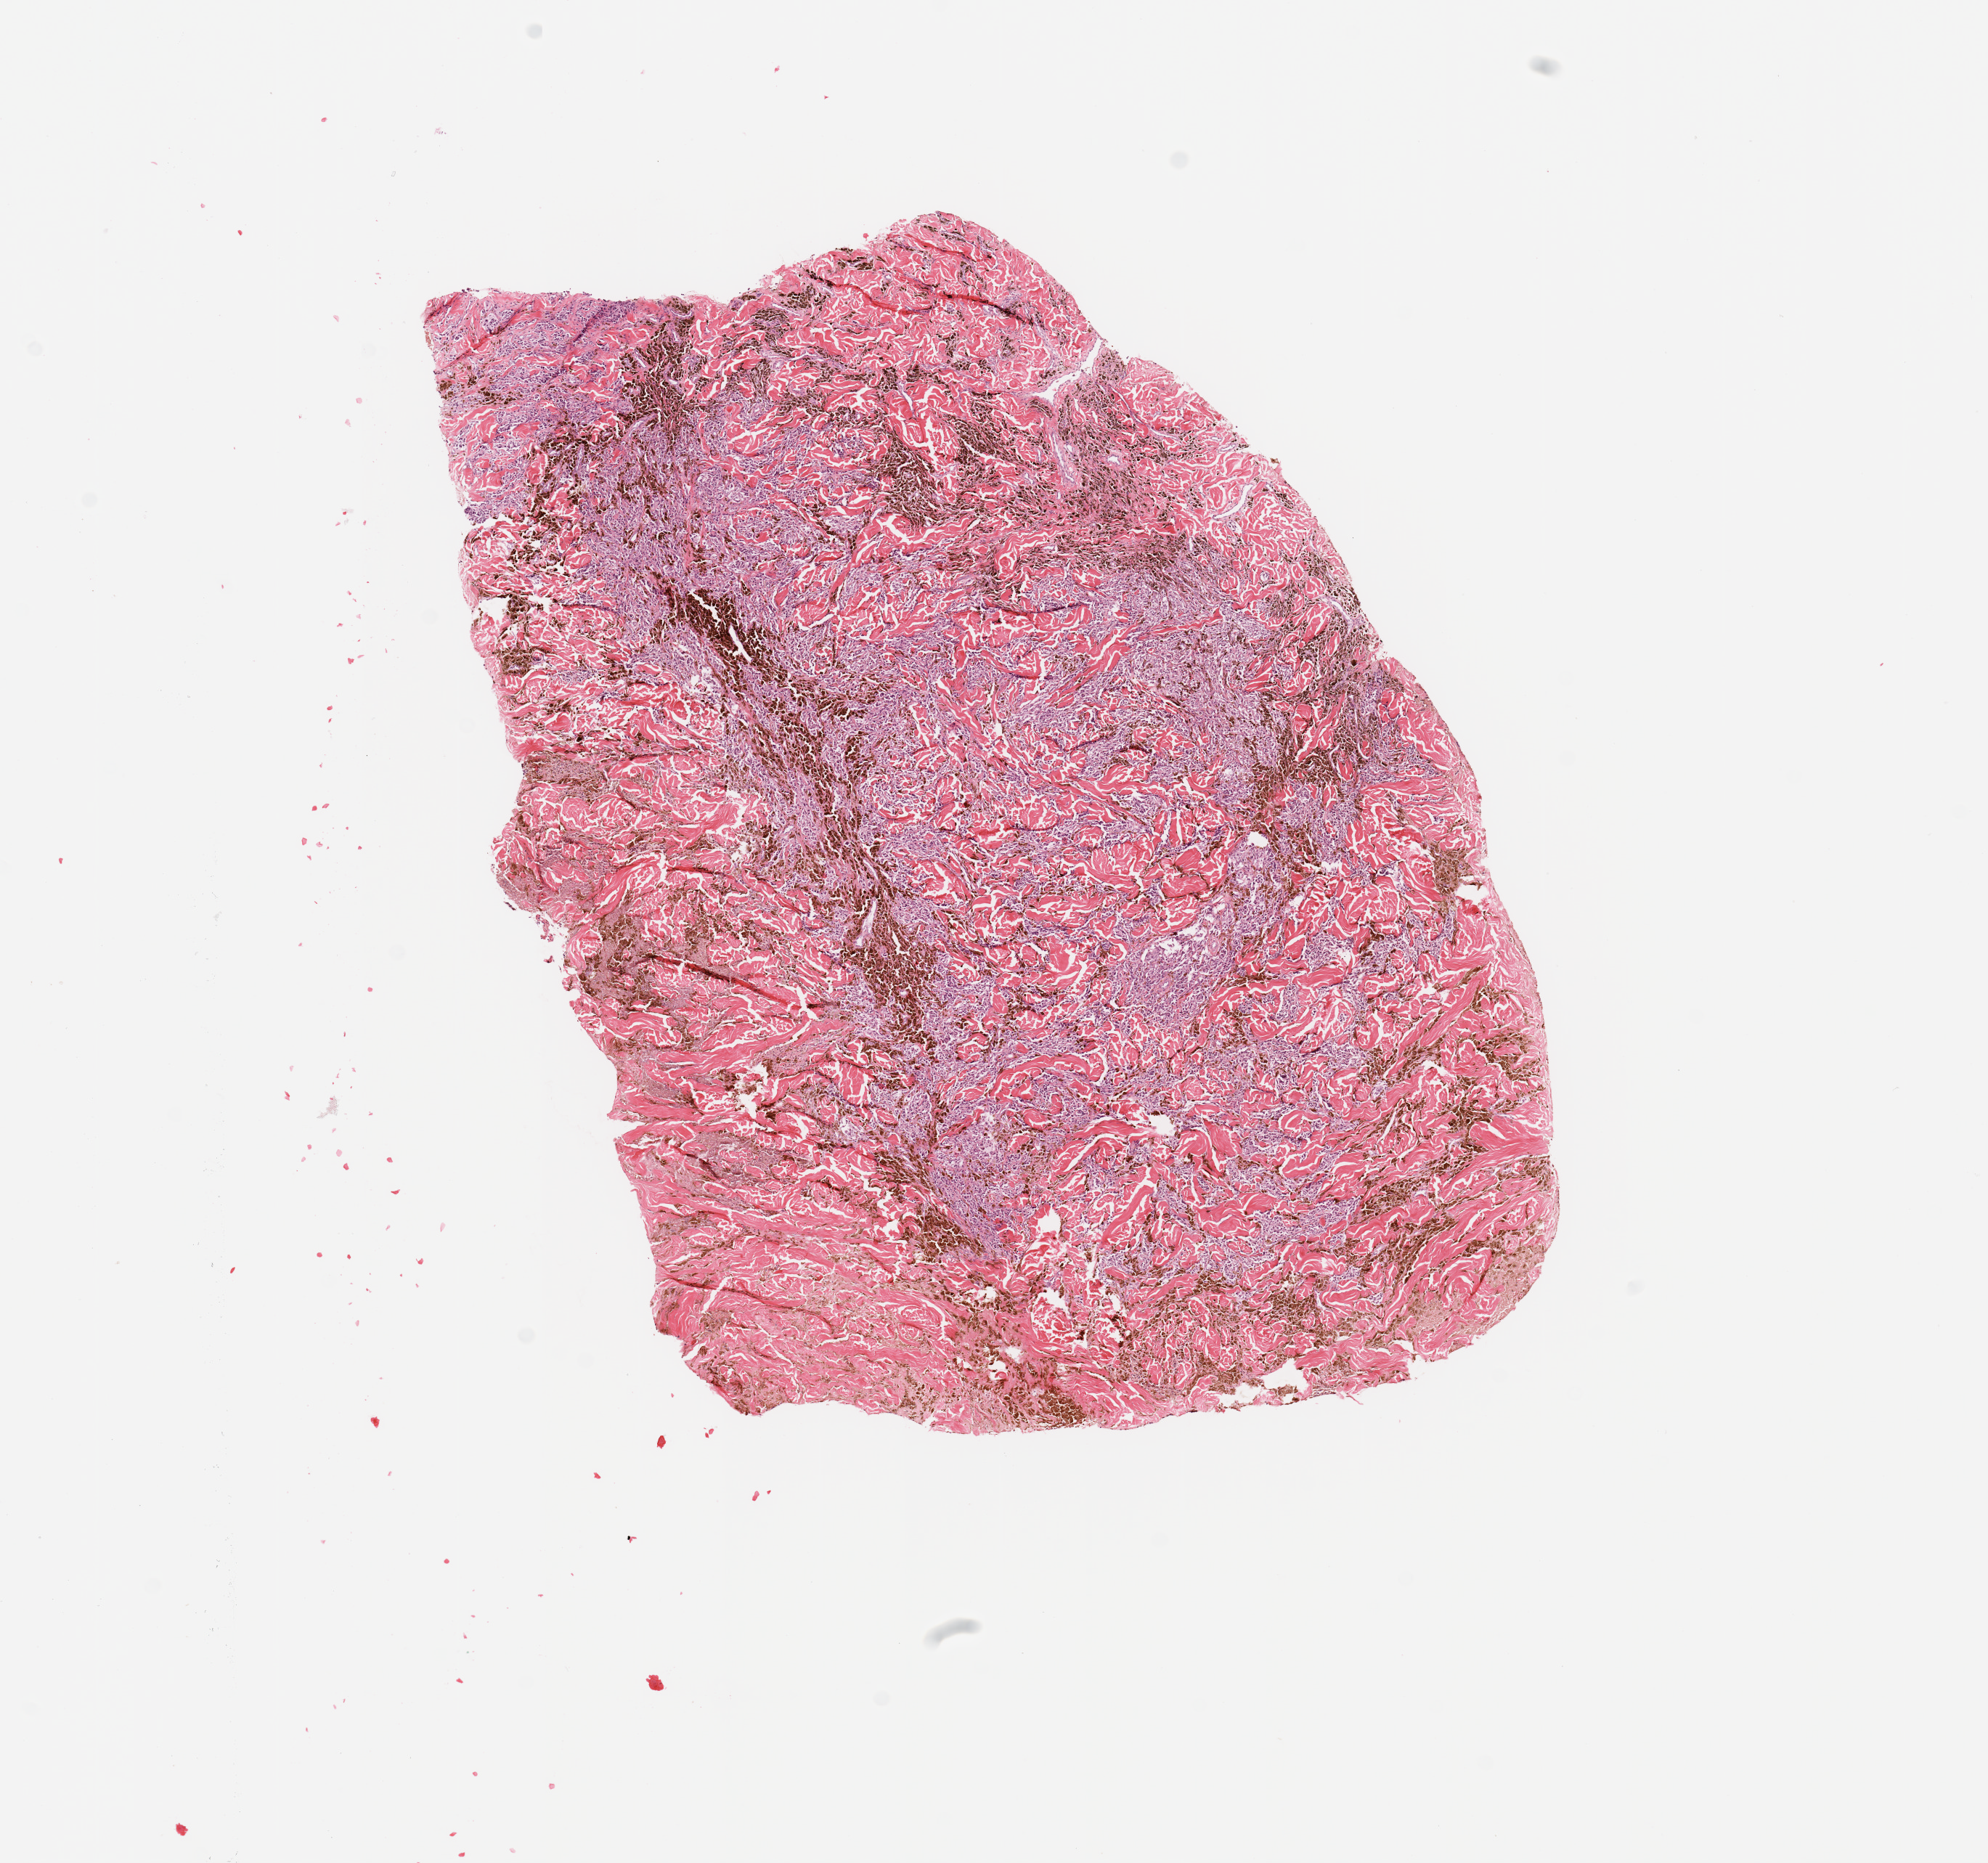
Hematoxylin and eosin (H&E) stained whole-slide image — a low-resolution overview of the entire scanned area, about 10.8 x 10.1 mm. Melanoma tumour tissue; sampled site not recorded. Female, 81 y/o.
Diagnosis: Malignant melanoma, NOS. AJCC pathologic stage: IIC. Primary tumour site (as recorded): trunk.